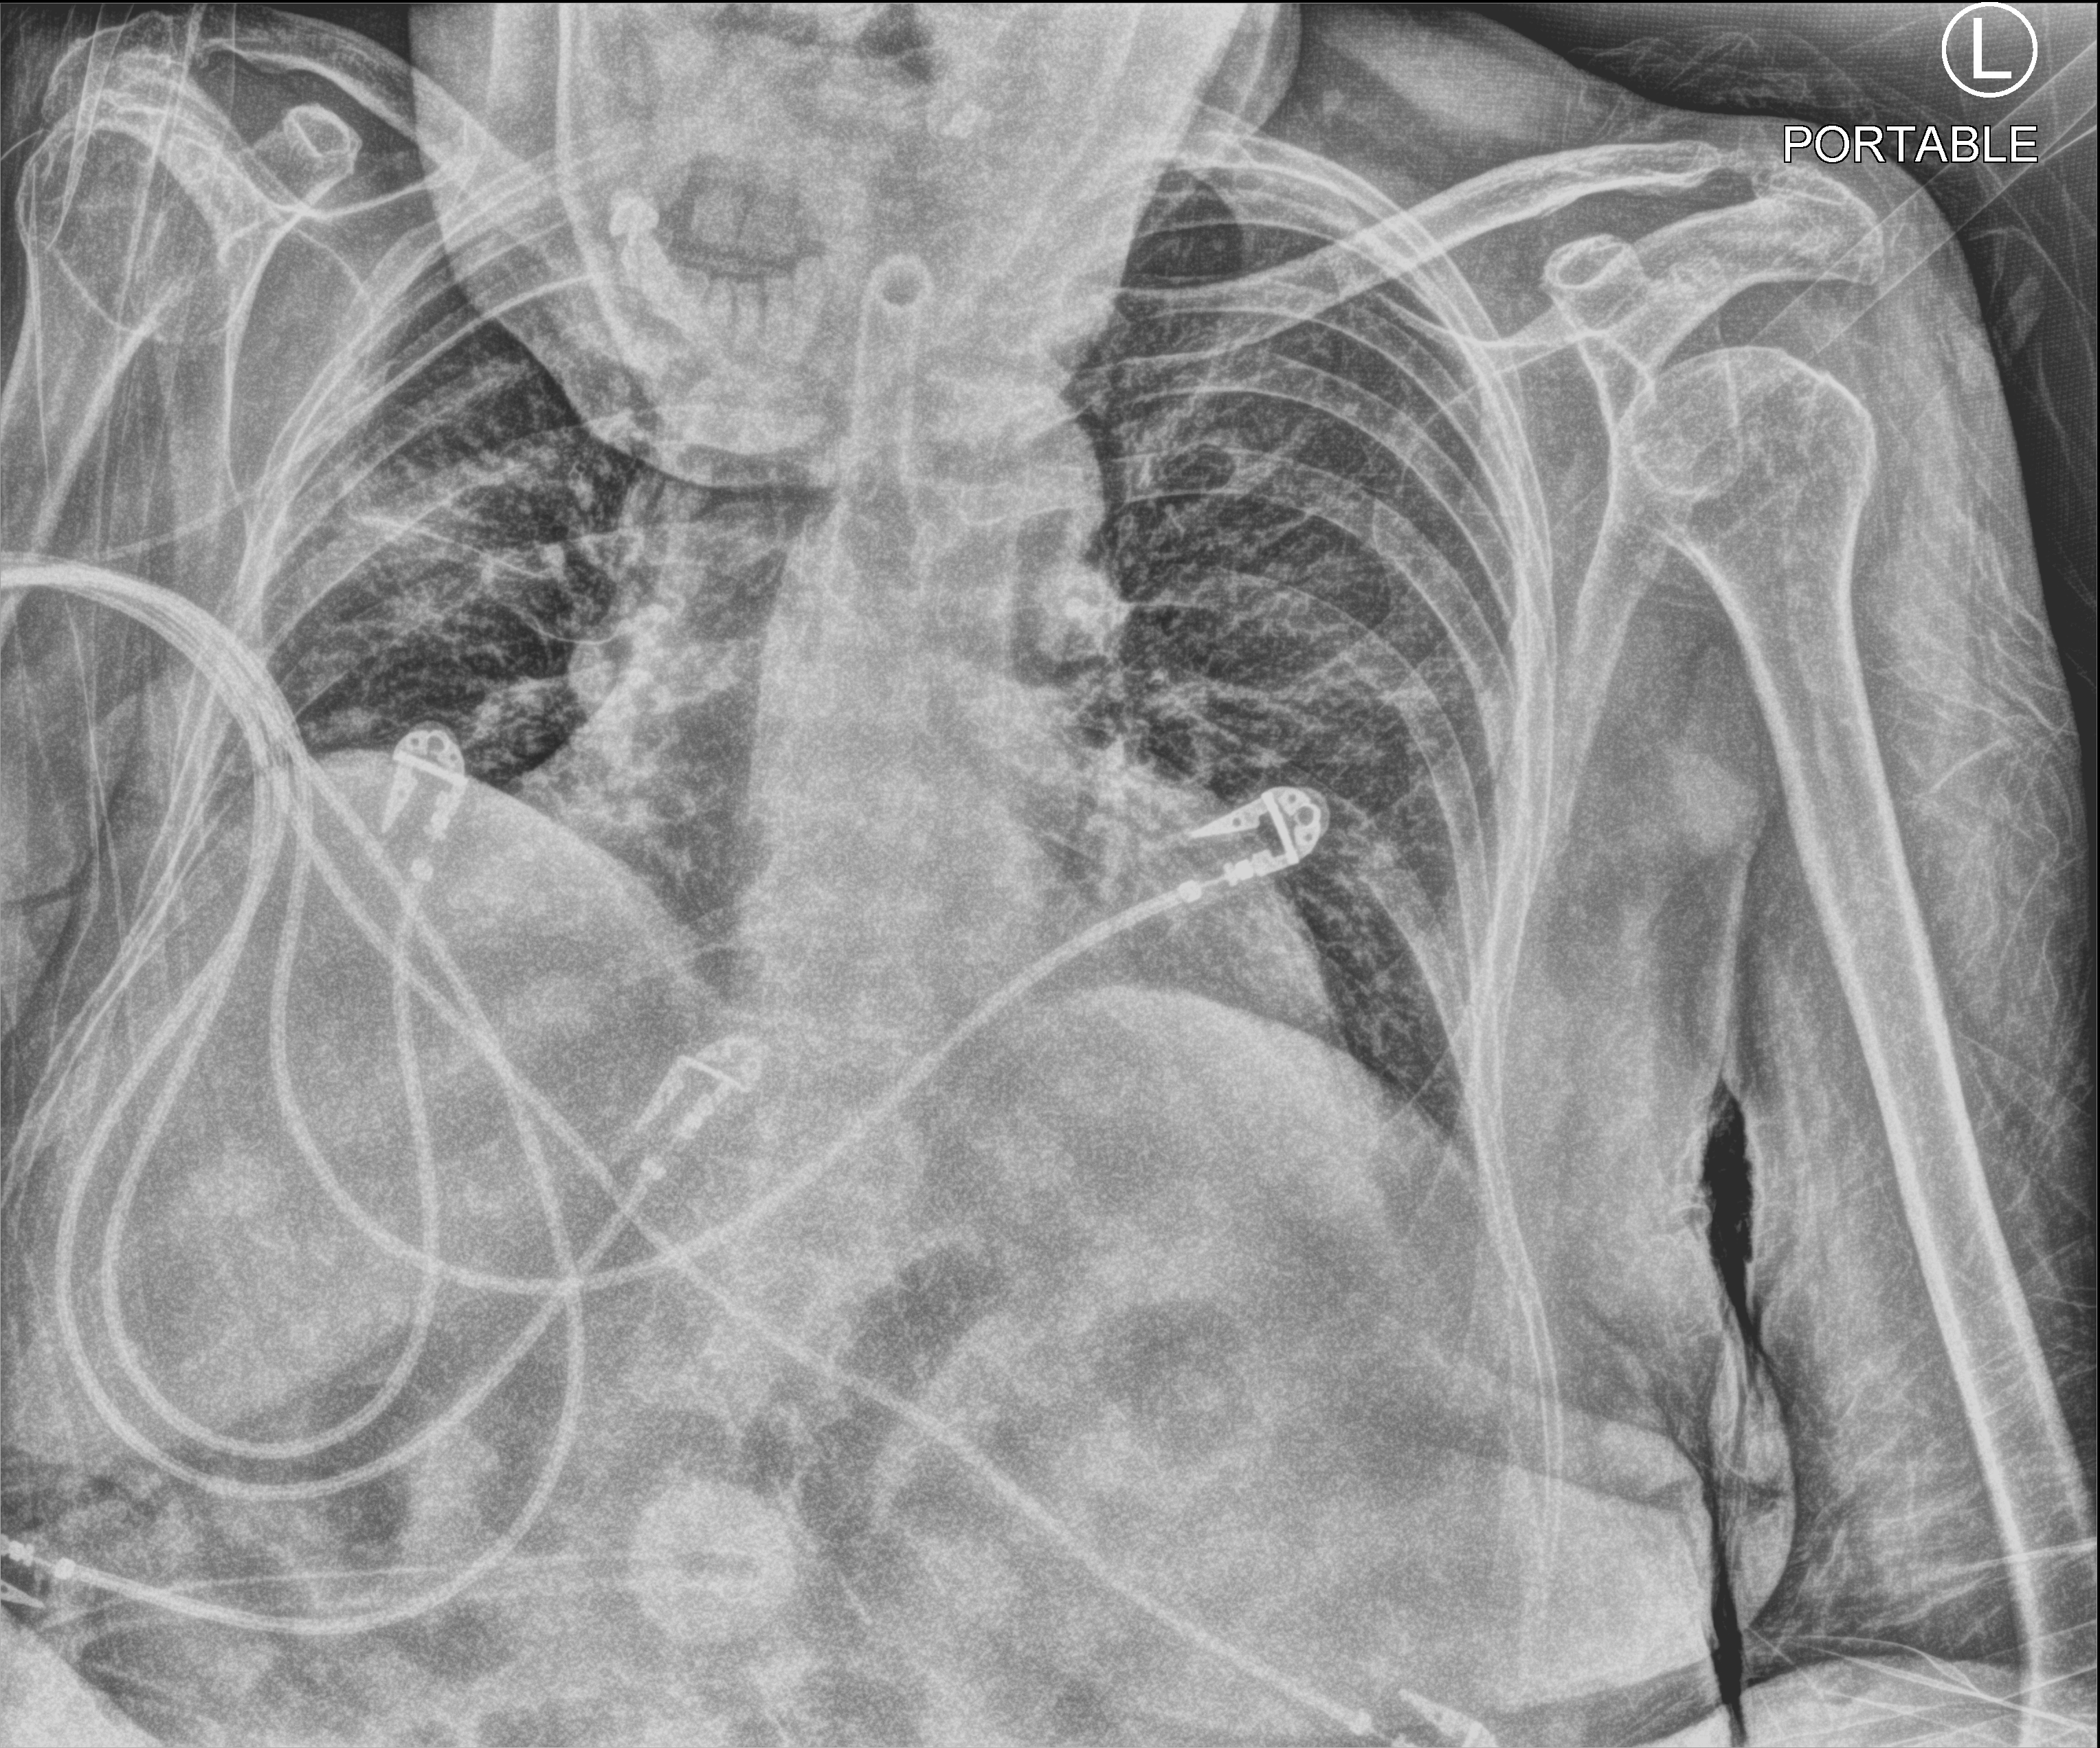
Chest X-ray (portable); anteroposterior (AP) projection. Female patient hospitalised with COVID-19, age 75–90 years.
Admission-level facts for this patient (not findings on this image; timing relative to this image not recorded):
- mechanically ventilated during this hospital stay: yes